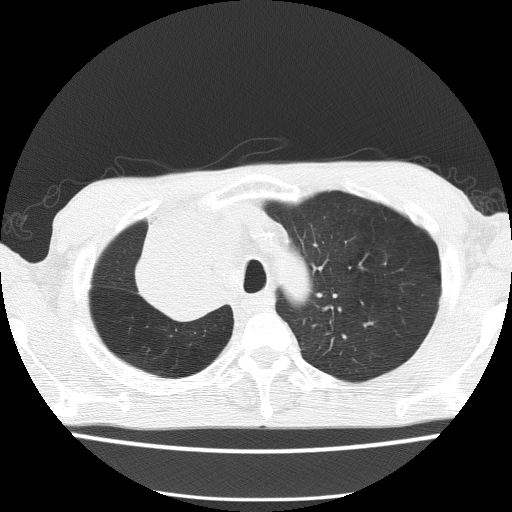
Low-dose screening chest CT, one axial slice. Slice 119 of 150 in the series (ordered by position). Reconstruction kernel FC51. 120 kVp. Lung window (W 1500 / L -600 HU). 512 × 512 image matrix, field of view 336 × 336 mm.
Structures marked on this image (expert manual segmentation):
- lesion 1 (tumor, hilum of right lung): box from (x=135, y=208) to (x=222, y=319) px